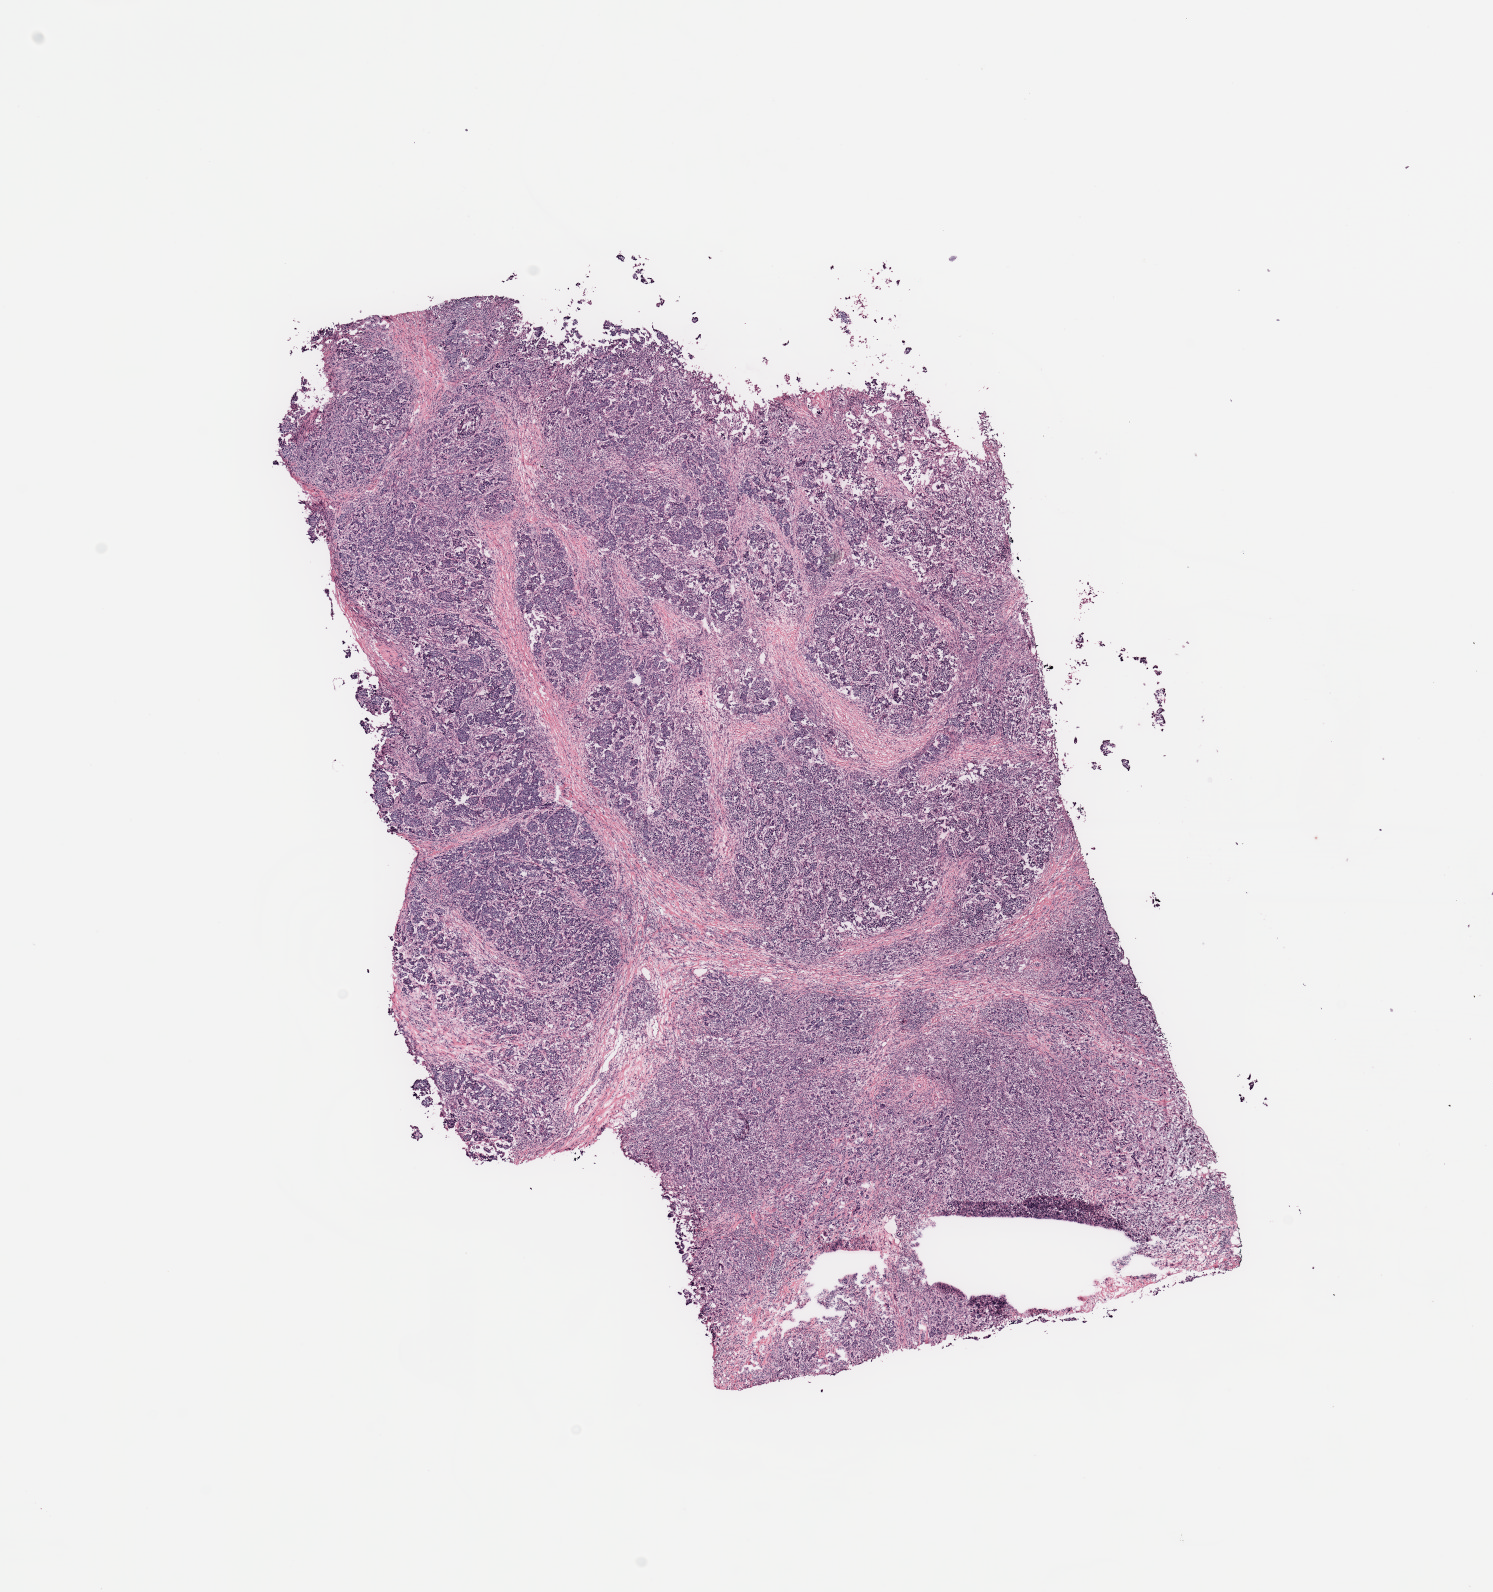
Hematoxylin and eosin (H&E) stained whole-slide image, a low-resolution overview of the entire scanned area, about 11.8 x 12.6 mm (acquisition: 20x scan). 86-year-old female patient.
* specimen: breast, tumour tissue